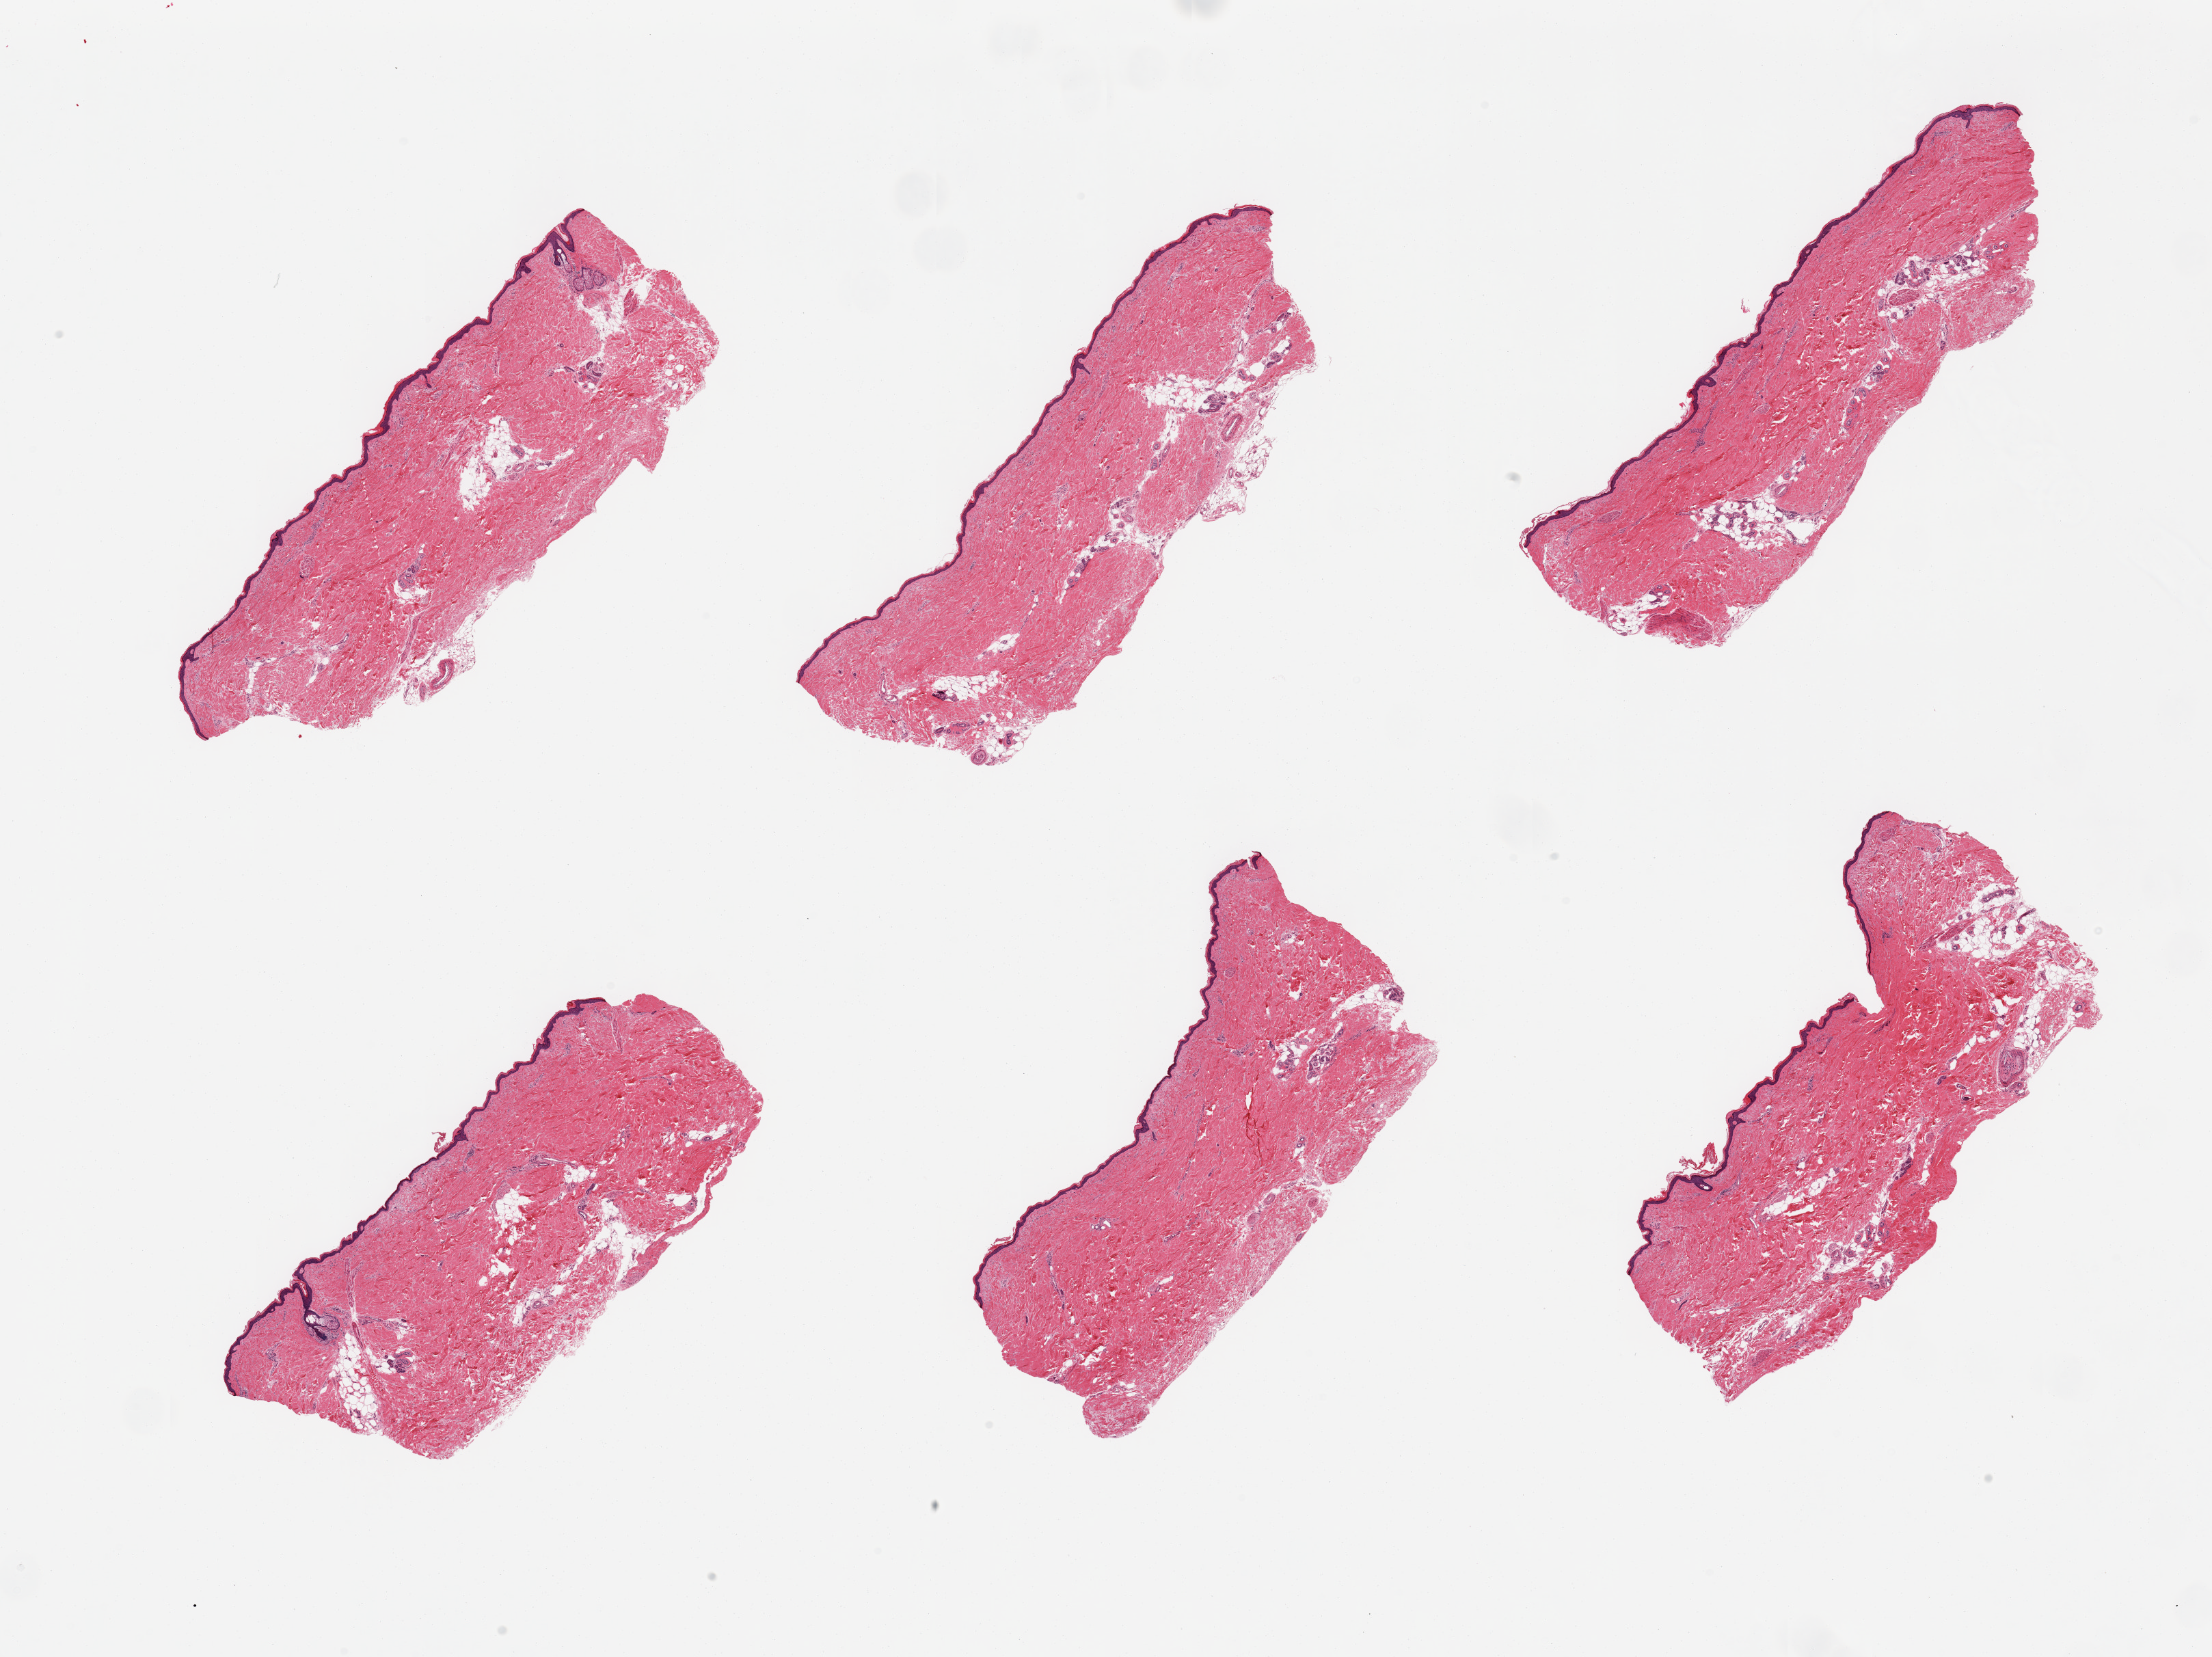
Digitized haematoxylin and eosin-stained section, low-resolution overview of the scanned area, about 25.6 x 19.2 mm; PAXgene-fixed, paraffin-embedded tissue; target tissue: skin of lower leg; donor tissue sample. Donor: male.
Reviewer comment on this tissue sample: 6 pieces, minimal dermal fat, squamous epithelium is ~40-50 microns.